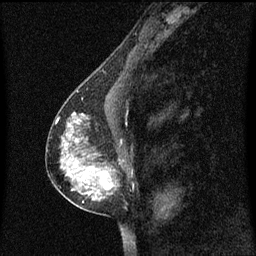
Breast MRI (dynamic contrast-enhanced), one sagittal slice. Position 36 of 60 along the scan axis. Dynamic contrast-enhanced series, image 2 of 3 at this slice position (ordered by acquisition). 1.5 T. TE 4.2 ms, TR 8.4 ms. 2 mm slice thickness. 256 × 256 image matrix. Patient: female, 40 years. From the clinical record (not read from this slice): setting: breast cancer imaged before/during neoadjuvant chemotherapy; receptor status: triple-negative.
Annotated regions visible in this slice (semi-automatic segmentation, software-assisted and operator-edited):
- analysis volume of interest (the breast-tissue region the enhancement analysis was run in; not a lesion): bounding box <60,104,125,213> (left, top, right, bottom; pixels)
- tumour enhancement mask (voxels above the 70 % enhancement threshold inside the analysis volume of interest): <70,126,113,195>